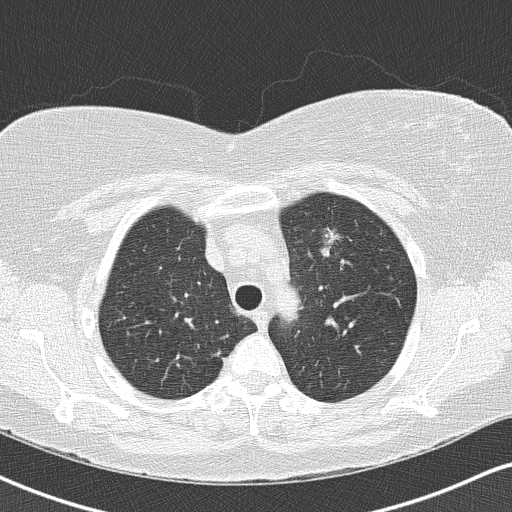
Low-dose screening chest CT, one axial slice. Slice 115 of 146 in the series (ordered by position). Reconstruction kernel B50f. Lung window (W 1500 / L -600 HU). 2 mm slice thickness. 512 × 512 image matrix.
Annotated regions visible in this slice (outlined manually by an expert reader):
- lesion 1 (tumor, upper lobe of left lung): bounding box [x1, y1, x2, y2] px = [319, 227, 343, 258]